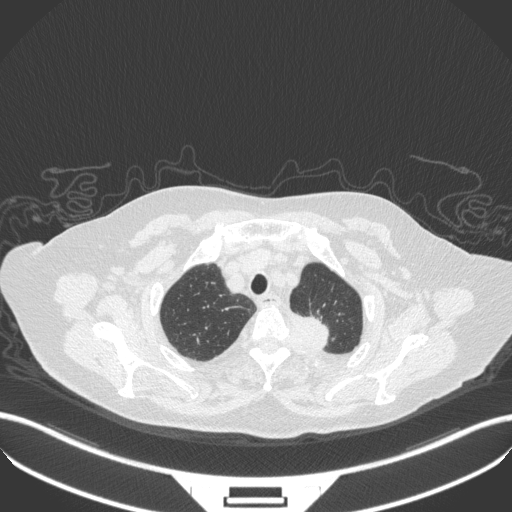
Chest CT, one axial slice. Position 297 of 353 along the scan axis. Reconstruction kernel B31f. 100 kVp. Lung window (W 1500 / L -600 HU). 1 mm slice thickness. 512 × 512 image matrix, field of view 400 × 400 mm. Patient: female, 81 years. Case-level facts recorded for this patient, not image findings: clinical TNM (as recorded): T2a N0 M0.
Annotated regions visible in this slice (bounding box drawn by a radiologist):
- lung tumour (recorded histology: adenocarcinoma): bounding box <284,310,339,354> (left, top, right, bottom; pixels)